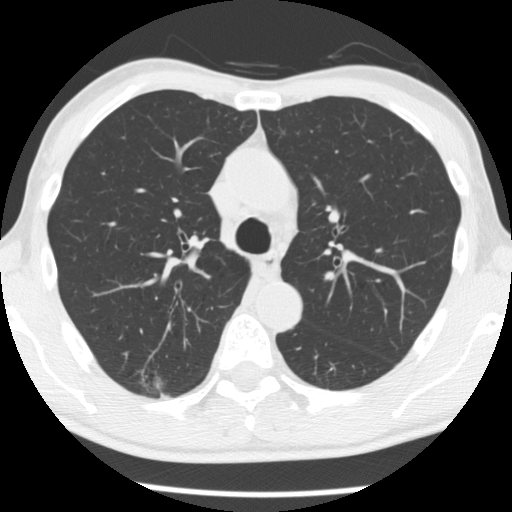
Low-dose screening chest CT, axial slice; first (baseline) screen; lung window (W 1500 / L -600 HU); 2.5 mm slice thickness; slice 91 of 277 in the series; 512 × 512 image matrix. Male participant, aged 66 years at enrolment. Former smoker at enrolment.
Expert-annotated lung lesion, bounding box [x1, y1, x2, y2] px = [129, 356, 192, 407]. The screening reader recorded 4 non-calcified nodules or masses ≥4 mm on this exam (right upper lobe, right upper lobe, right upper lobe, left lower lobe); which of them this box marks is not recorded. Official screen result: positive, change unspecified: nodule(s) >= 4 mm or enlarging nodule(s), mass(es), or other non-specific abnormalities suspicious for lung cancer.